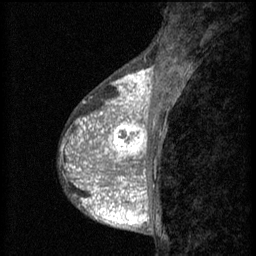
Breast MRI (dynamic contrast-enhanced), one sagittal slice; slice 24 of 60 in the series (ordered by position); 3 images stored at this slice position (order not interpretable as contrast timing); 1.5 T; TE 4.2 ms, TR 8.2 ms; 2 mm slice thickness; 256 × 256 image matrix, field of view 180 × 180 mm. Patient: female, 38 years.
Structures marked on this image (semi-automatically segmented with operator editing):
- analysis volume of interest (the breast-tissue region the enhancement analysis was run in; not a lesion): bounding box <92,112,152,171> (left, top, right, bottom; pixels)
- tumour enhancement mask (voxels above the 70 % enhancement threshold inside the analysis volume of interest): <92,112,148,171>